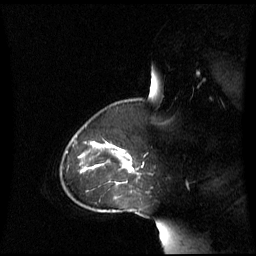
Breast MRI (dynamic contrast-enhanced), one sagittal slice. Position 46 of 60 along the scan axis. Dynamic contrast-enhanced series, image 2 of 3 at this slice position (ordered by acquisition). 1.5 T. TE 4.2 ms, TR 8.4 ms. 256 × 256 image matrix, field of view 270 × 270 mm. Patient: female, 43 years. Case-level facts recorded for this patient, not image findings: setting: breast cancer imaged before/during neoadjuvant chemotherapy; receptor status: triple-negative.
Annotated regions visible in this slice (semi-automatically segmented with operator editing):
- analysis volume of interest (the breast-tissue region the enhancement analysis was run in; not a lesion): box from (x=69, y=137) to (x=142, y=198) px
- tumour enhancement mask (voxels above the 70 % enhancement threshold inside the analysis volume of interest): (x=105, y=142)–(x=131, y=172)